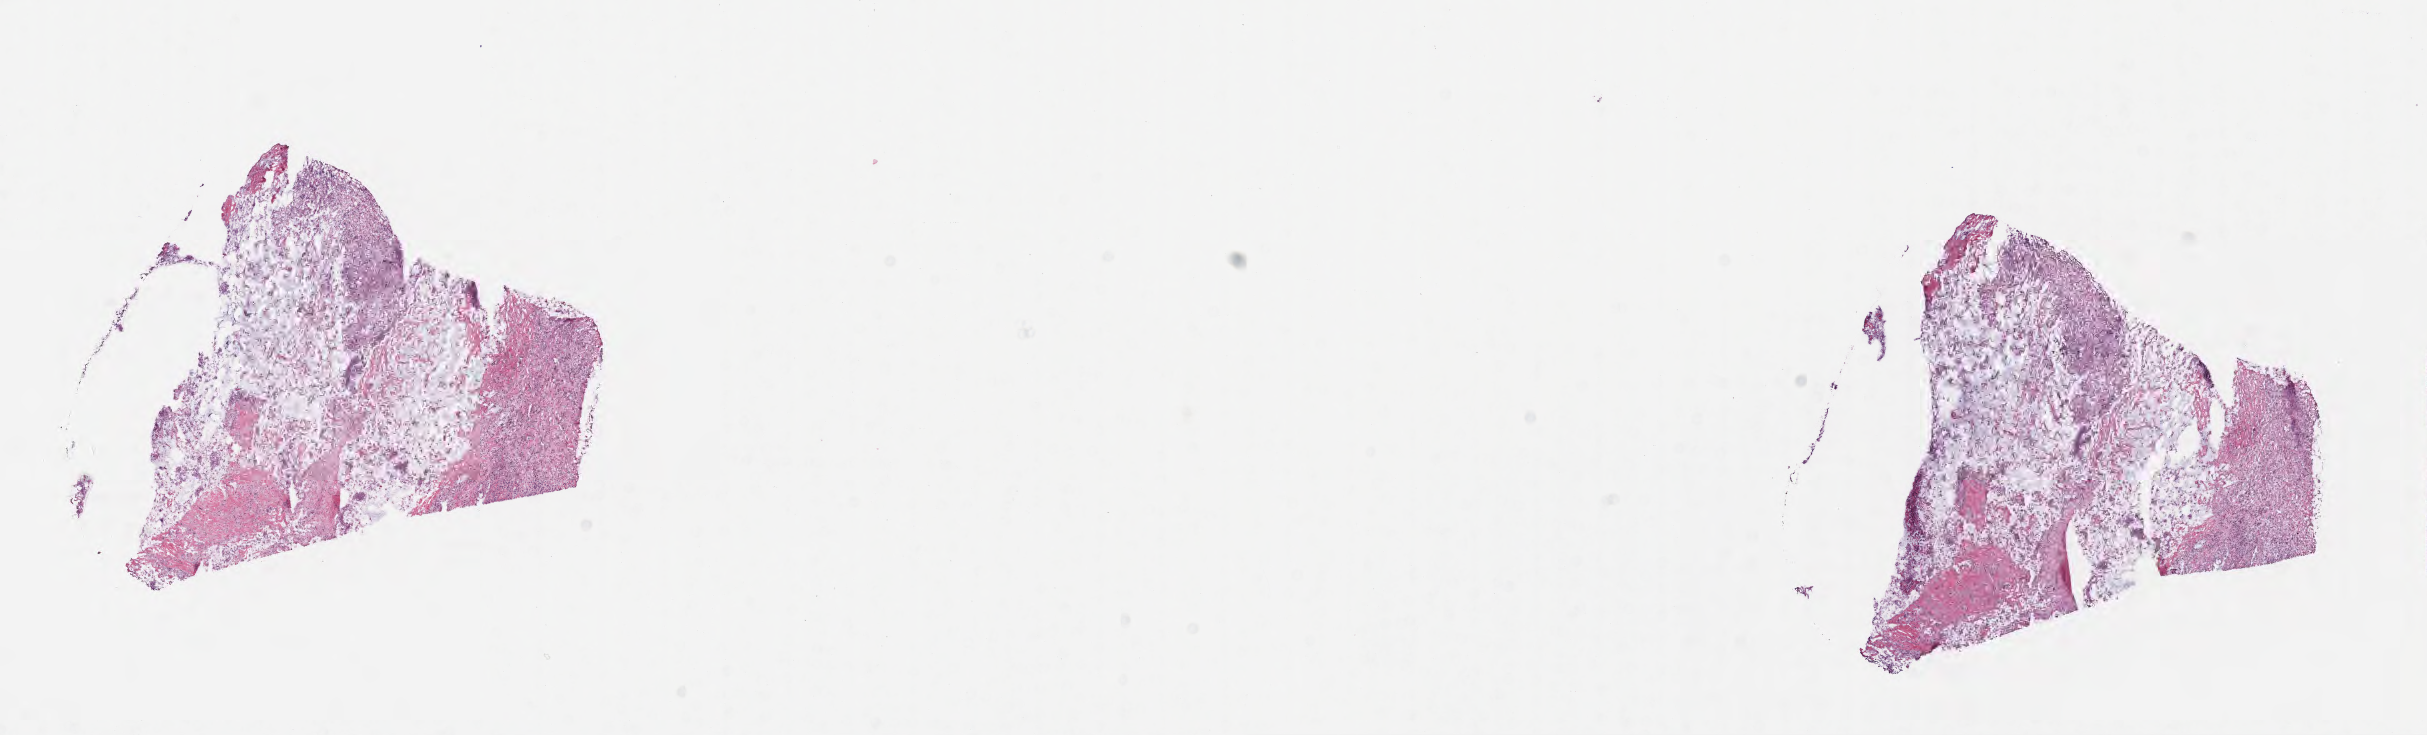
Whole-slide image, haematoxylin and eosin stain — whole scanned area (about 19.6 x 5.9 mm) shown as a low-resolution overview; cryosection; metastatic tumor tissue, resected from liver. Patient: female, age at initial diagnosis 51 years. Composition of this section per pathologist review: tumor cells 68%, tumor nuclei 92%, stromal cells 25%, necrosis 7%, normal cells 0%. Infiltration values recorded for this section: lymphocyte infiltration 4%, monocyte infiltration 1%, neutrophil infiltration 0%.
Patient diagnosis (primary): Adenocarcinoma, NOS.